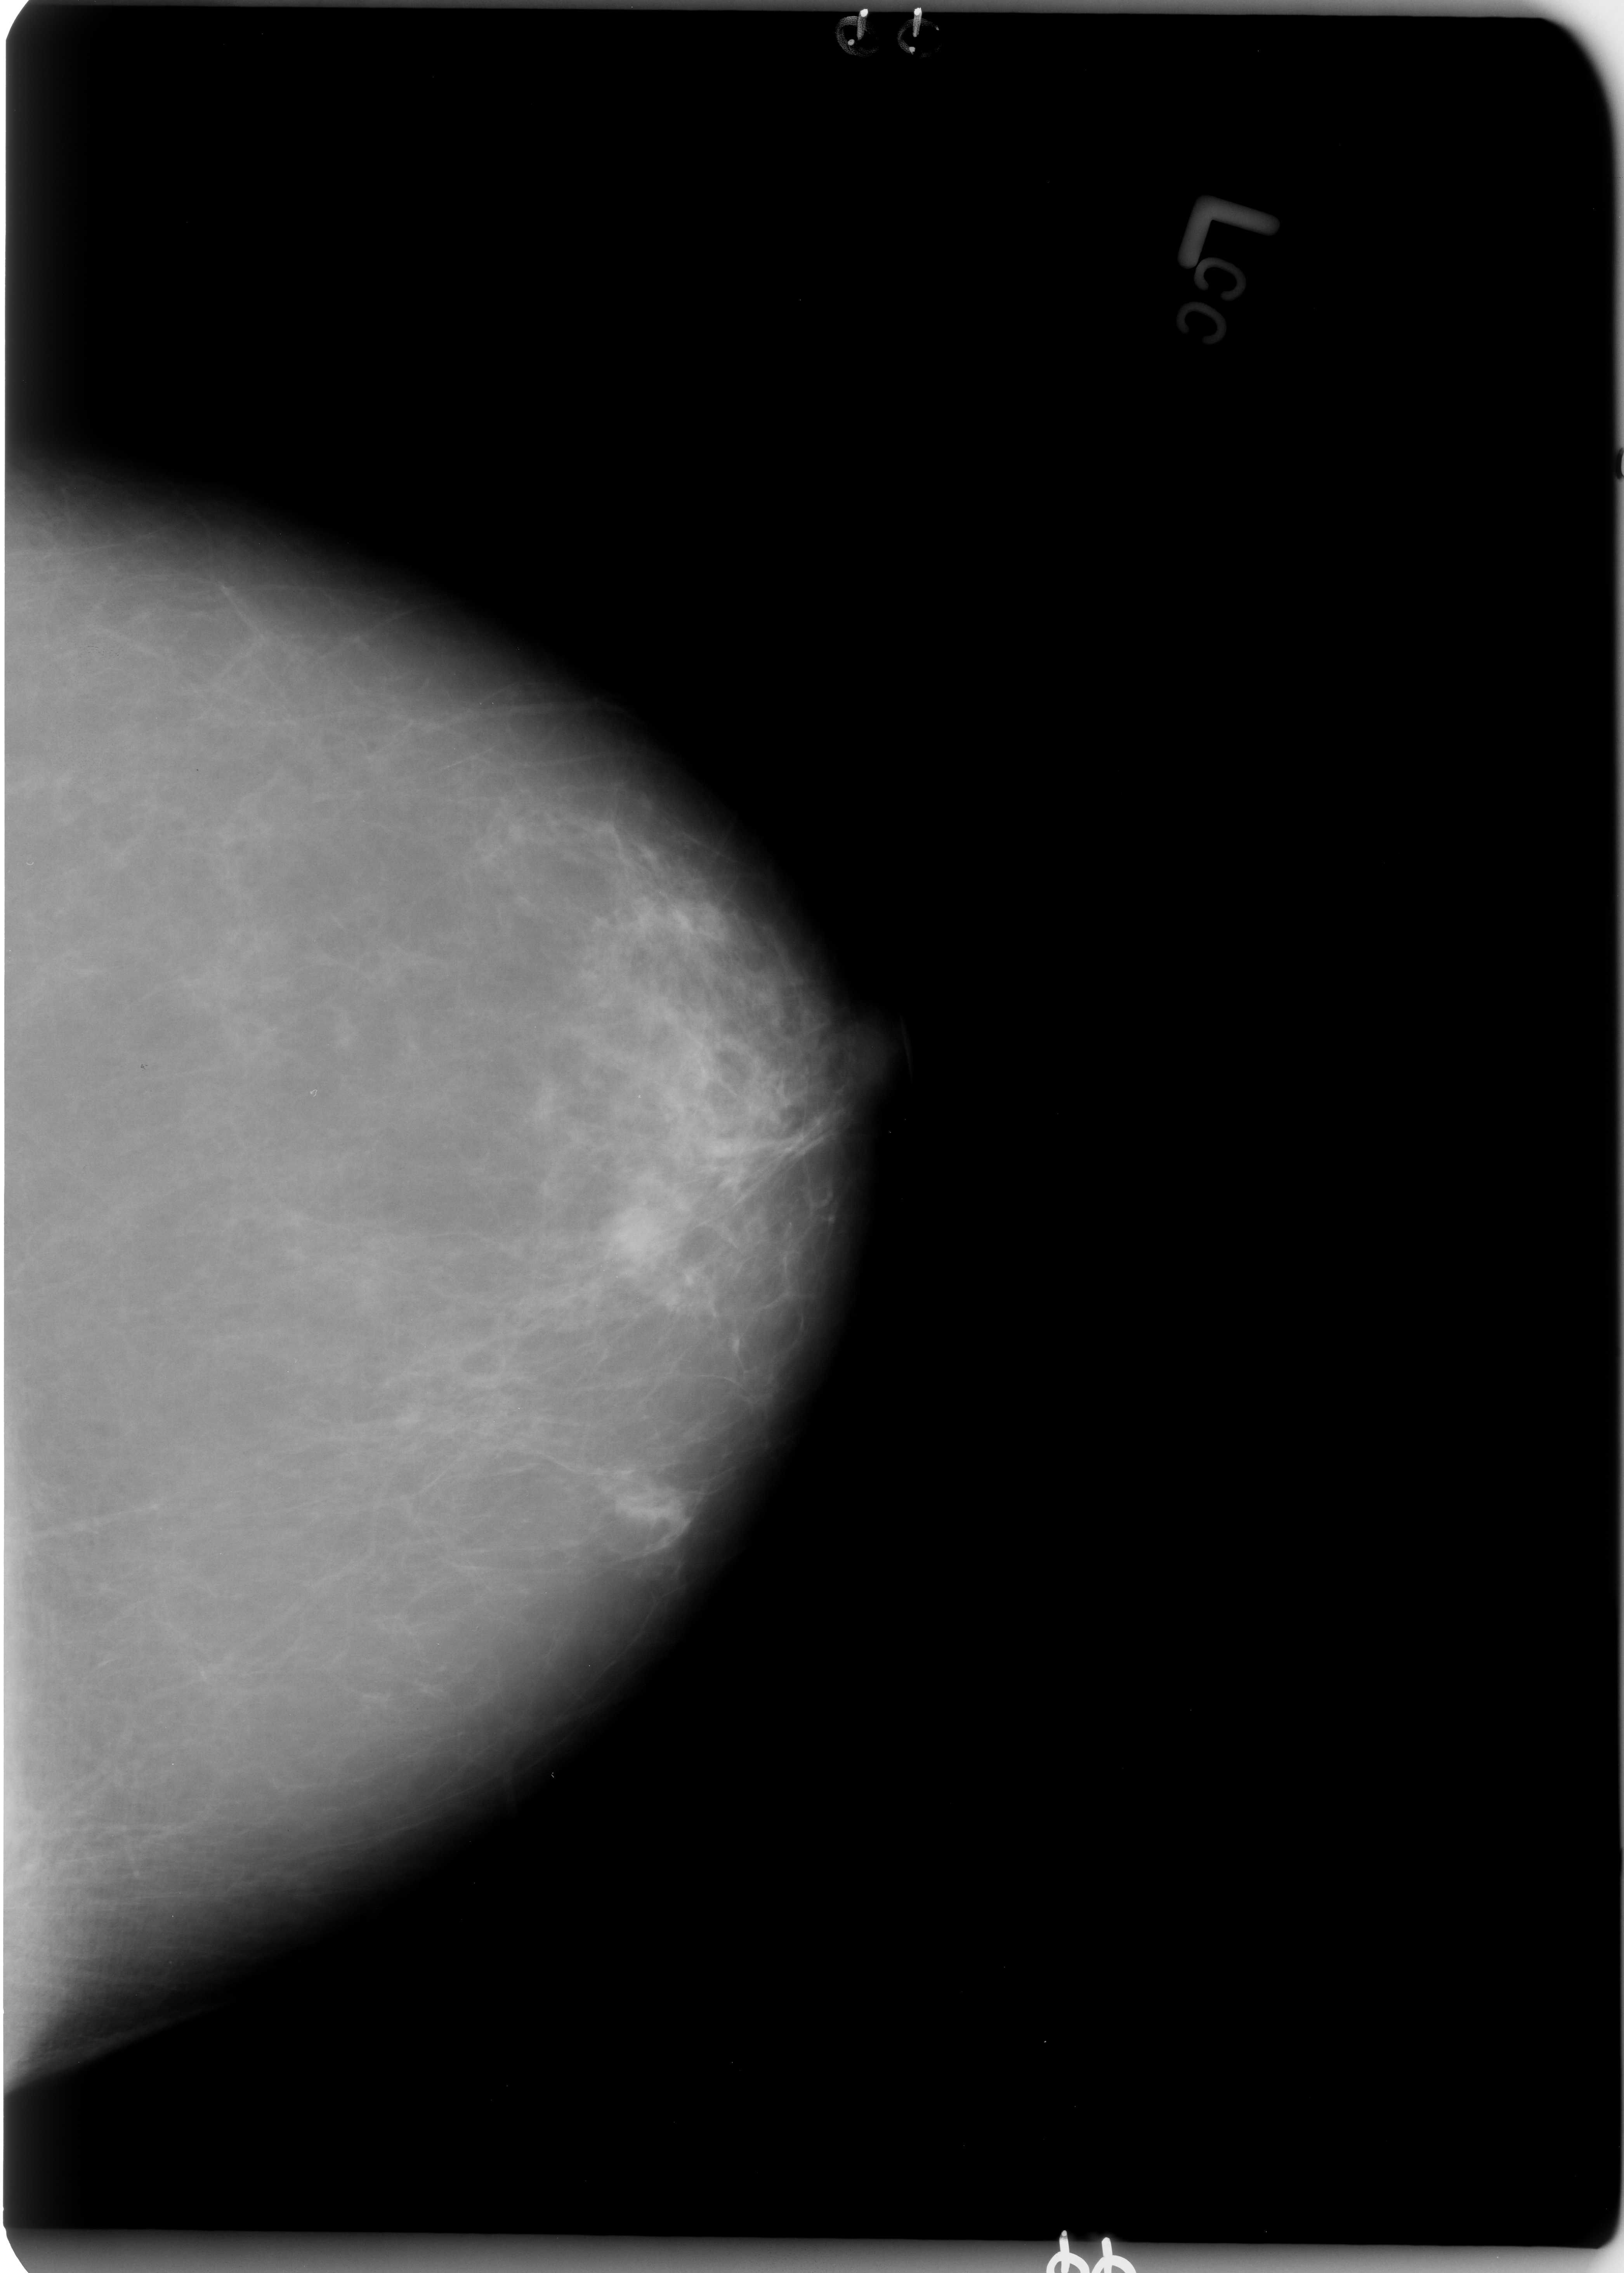
Scanned film-screen mammogram; left breast; craniocaudal (CC) view; BI-RADS breast density category 2 (scale 1–4).
Finding: mass, shape round, margins ill defined; BI-RADS assessment category 3; pathology result (as recorded, not read from the image): benign.